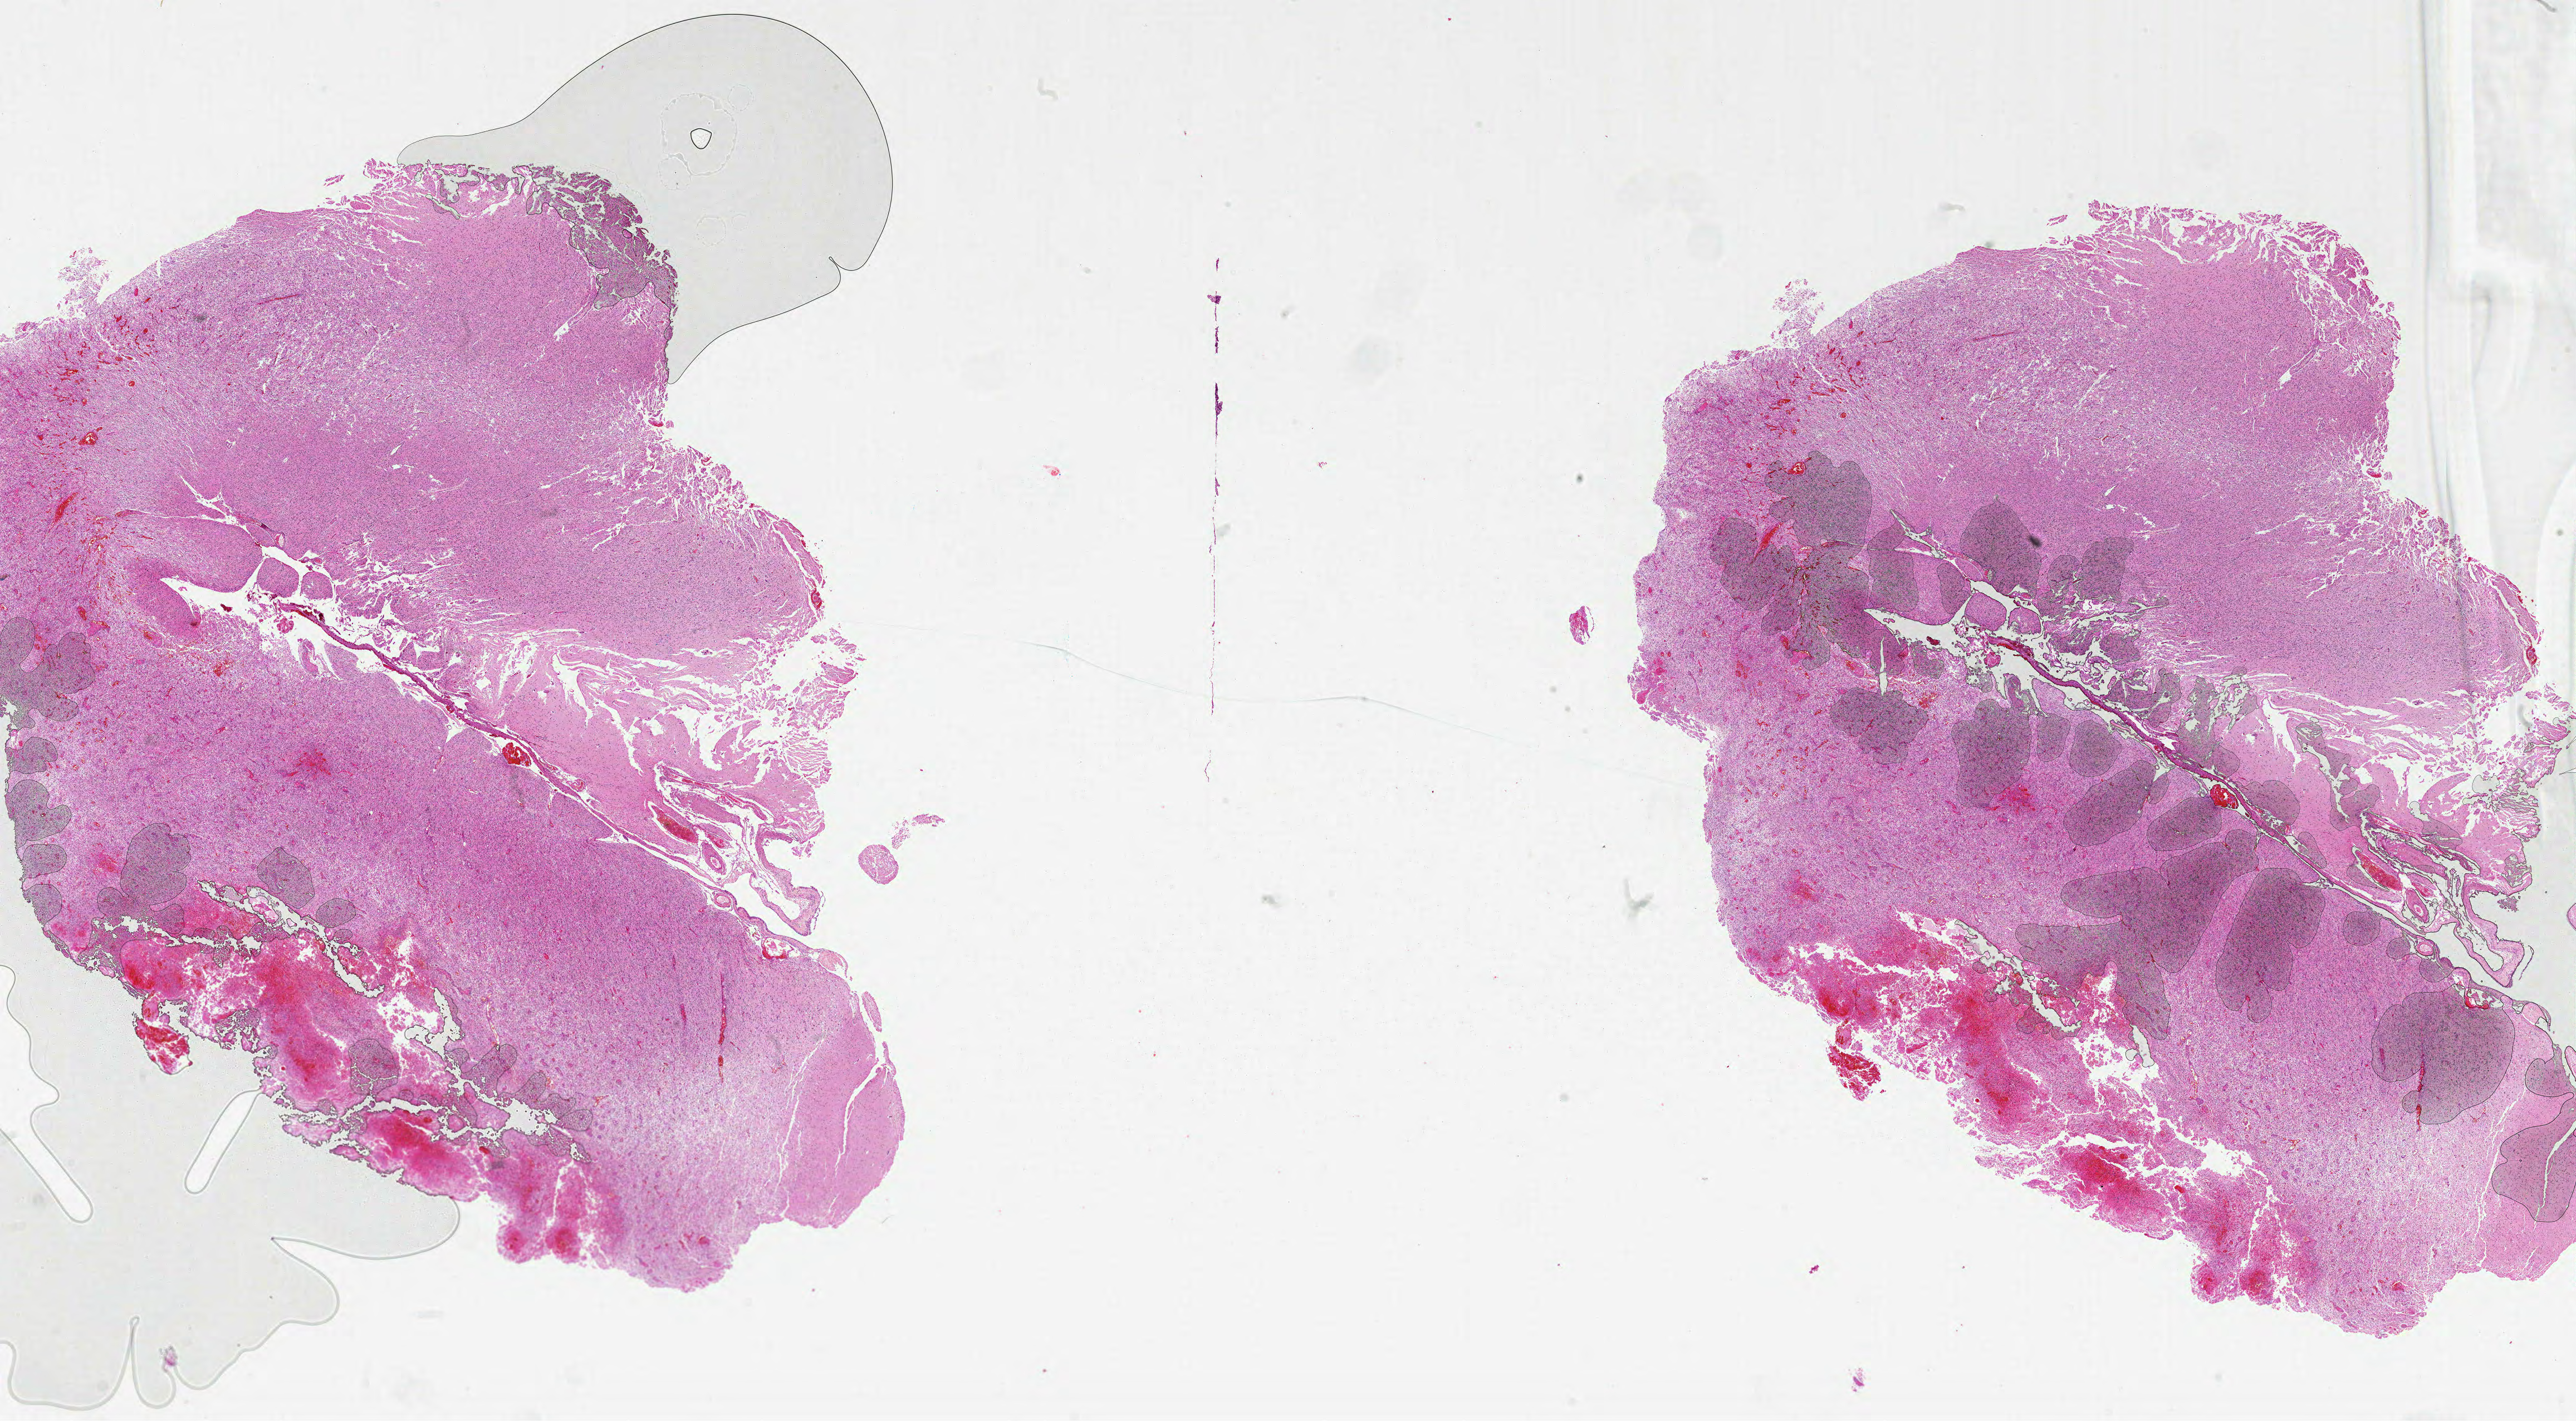
H&E whole-slide image, shown as a low-resolution overview of the whole scanned area (about 37.0 x 20.4 mm, slide scanned at 20x), formalin-fixed paraffin-embedded (FFPE) diagnostic section, brain, primary tumour sample. Male patient; age at initial diagnosis 53 years.
Pathologic diagnosis: Glioblastoma.